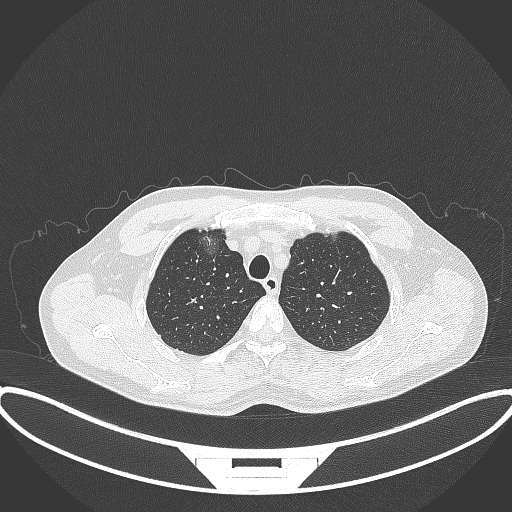
Chest CT, one axial slice. Position 301 of 395 along the scan axis. Lung window (W 1500 / L -600 HU). 1 mm slice thickness. 512 × 512 image matrix, field of view 424 × 424 mm. Patient: male, 60 years. From the clinical record (not read from this slice): clinical TNM (as recorded): T1c N0 M0.
Annotated regions visible in this slice (rectangle marked by the reading radiologist):
- lung tumour (recorded histology: adenocarcinoma): bounding box (x1, y1, x2, y2) in pixels: (195, 226, 226, 262)